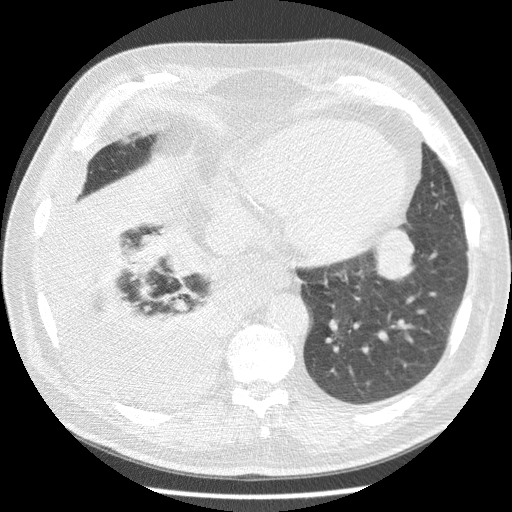
Axial slice from a low-dose chest CT screening exam. Third screening round (two years after baseline). Lung window (W 1500 / L -600 HU). 2.5 mm slice thickness. Standard (soft-tissue) reconstruction kernel (STANDARD). 120 kVp. Slice 60 of 180 in the series. Male participant, aged 63 years at enrolment. Current smoker at enrolment.
Lesion marked by an expert reader, bounding box (x1, y1, x2, y2) in pixels: (351, 224, 418, 294). Screening reader's record for this exam (one nodule recorded; not confirmed to be the boxed lesion): non-calcified nodule or mass ≥4 mm, left lower lobe, 34 × 31 mm, smooth margins, soft tissue attenuation, pre-existing on the prior screen: yes; interval growth: yes. Official screen result: positive, other. Later outcome: lung cancer diagnosed 30 days after this screen — squamous cell carcinoma, NOS, left lower lobe, stage IB (AJCC 6th edition), 48 mm at pathology.